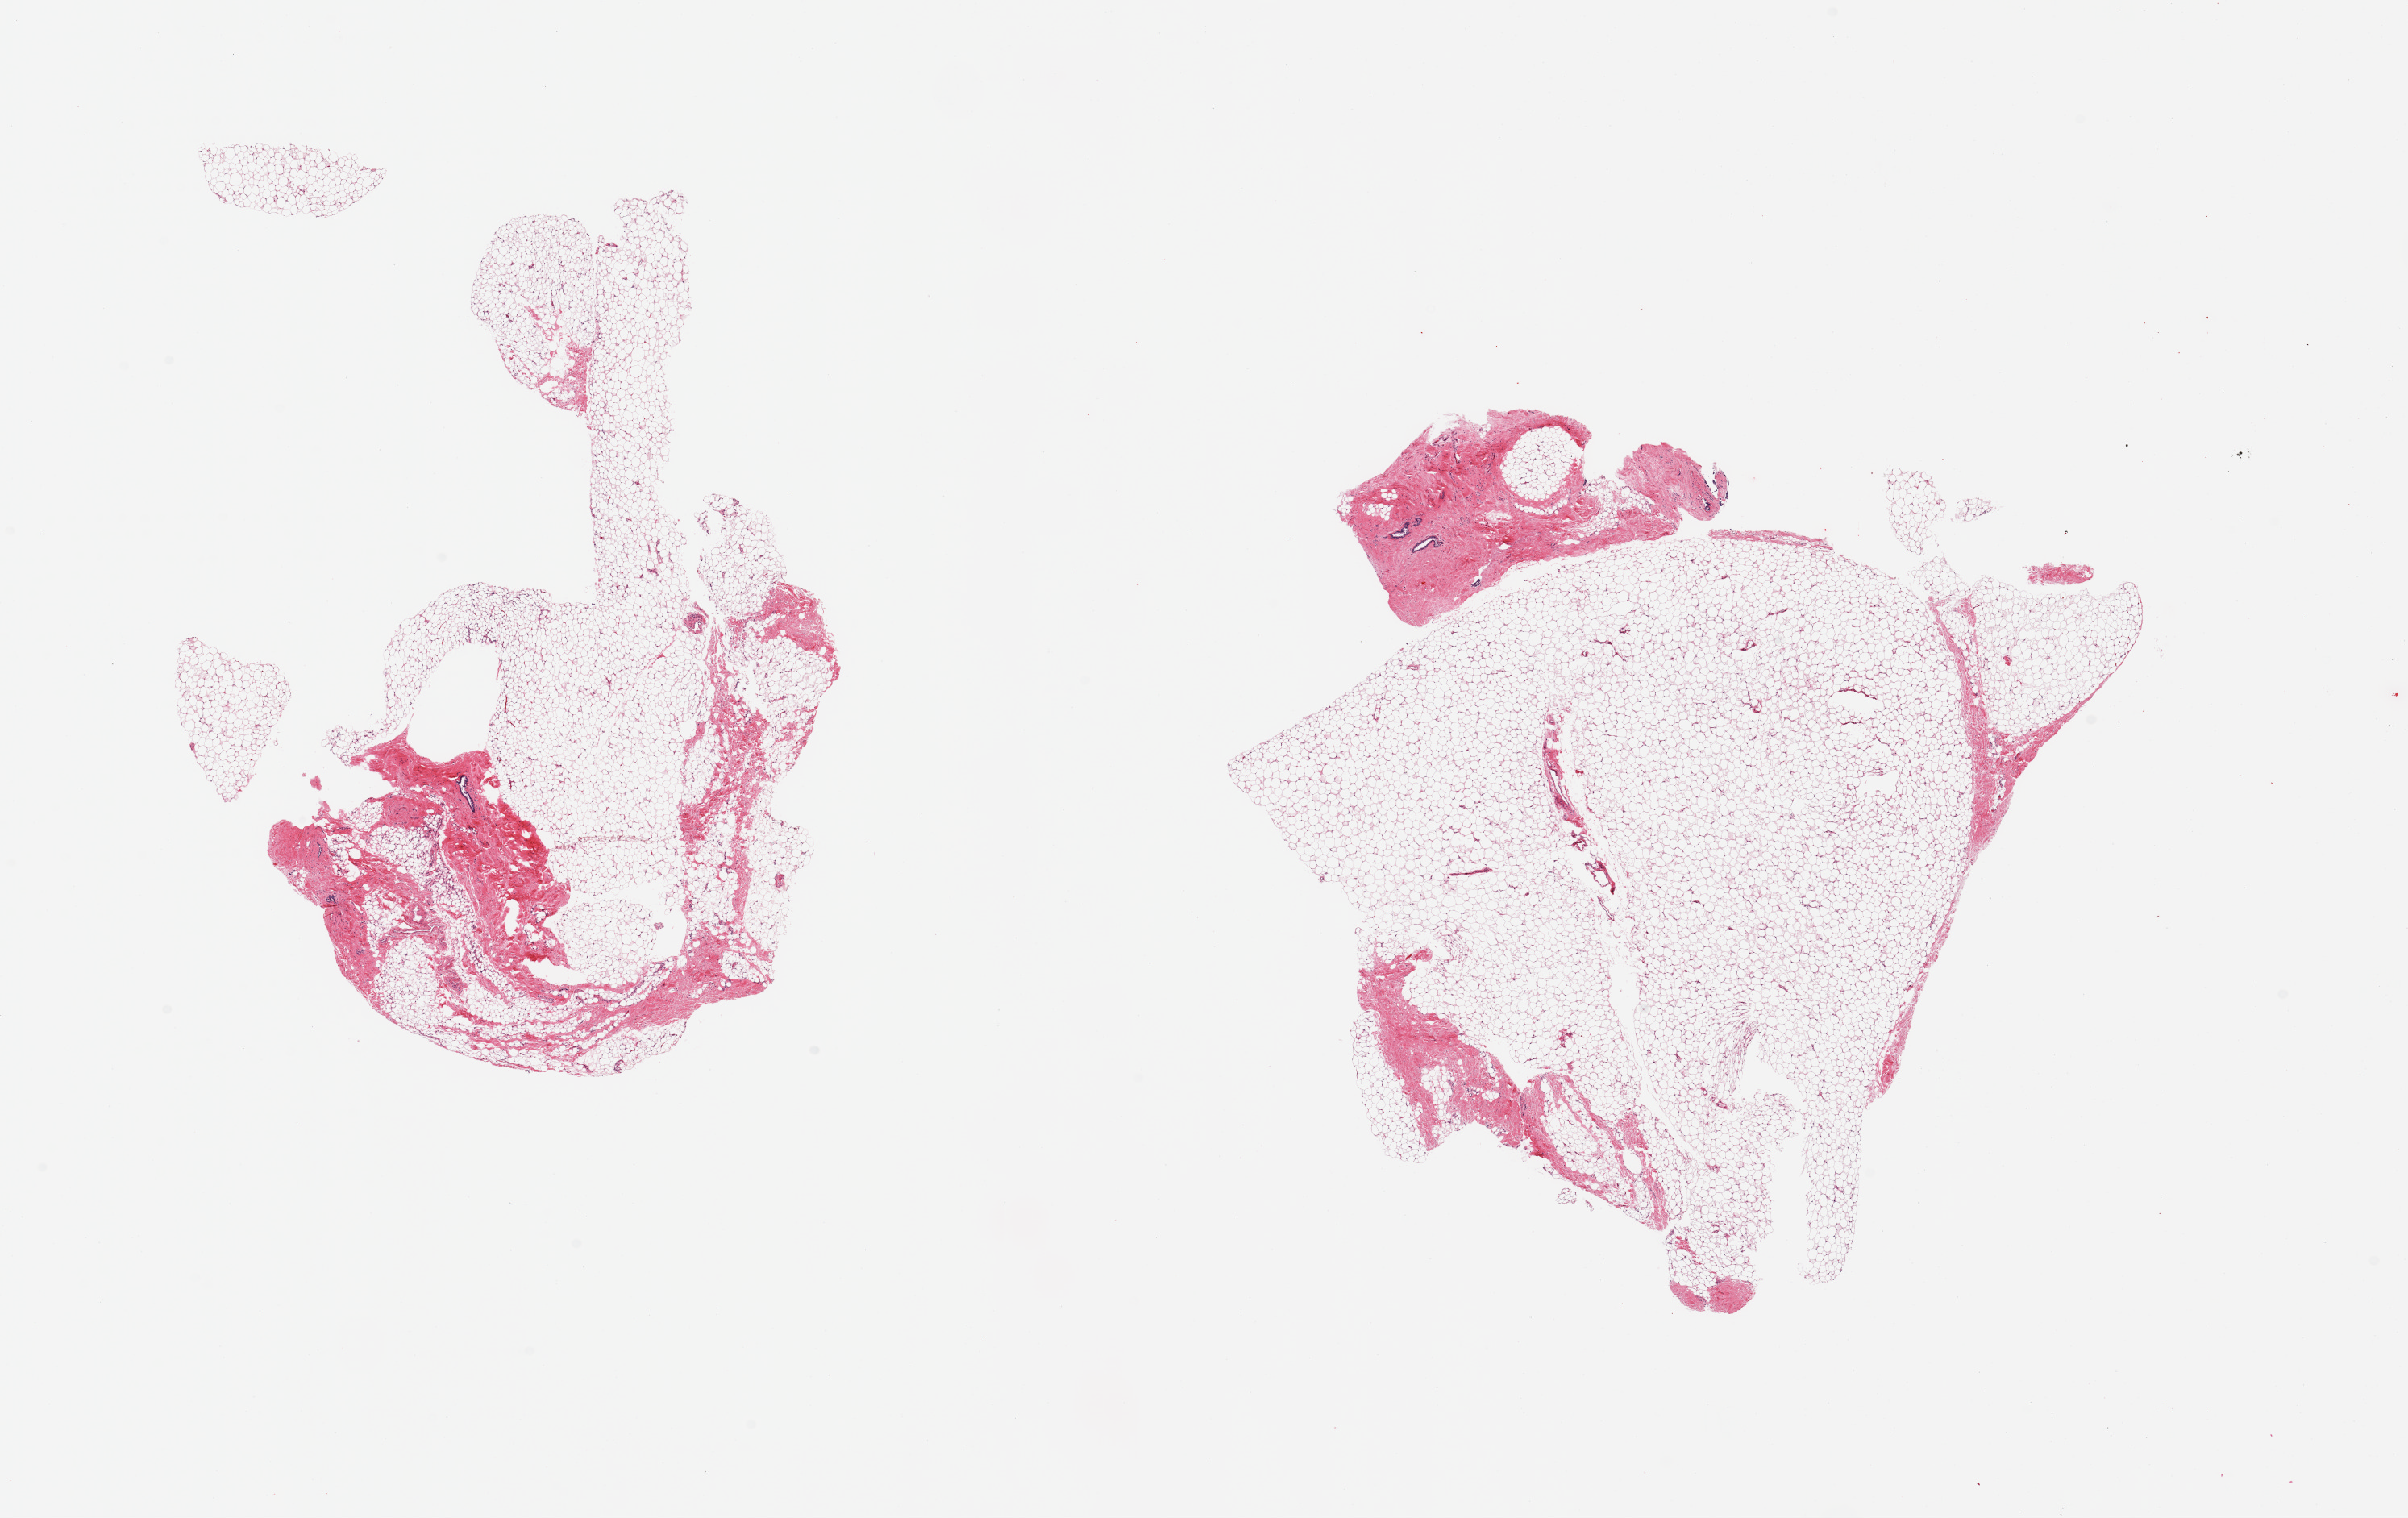
Whole-slide image, haematoxylin and eosin stain, brightfield, shown as a low-resolution overview of the whole scanned area (about 23.6 x 14.9 mm, slide scanned at 20x), PAXgene-fixed paraffin-embedded (PFPE) section, target tissue: breast, tissue donor sample.
- pathologist's review note for this sample: 2 pieces, fibroadipose elements, minute focus of ductal elements